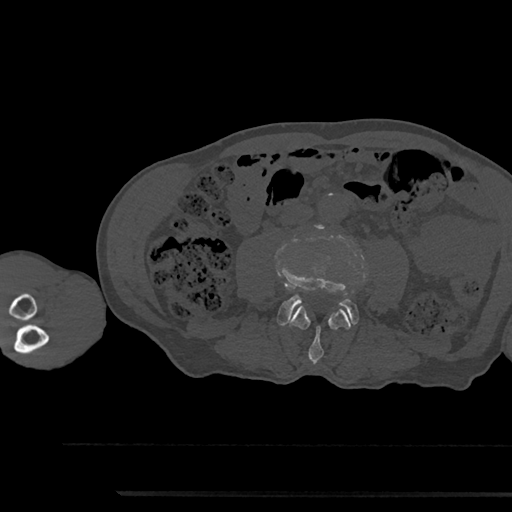
CT including the spine, one axial slice; slice 448 of 797 in the series (ordered by position); 120 kVp; bone window (W 1800 / L 400 HU); 0.5 mm slice thickness; 512 × 512 image matrix. Male patient, age 79 years. Case-level facts recorded for this patient, not image findings: primary cancer: prostate.
Annotated regions visible in this slice (semi-automatically segmented with operator editing):
- L3 vertebra: bounding box <289,305,351,364> (left, top, right, bottom; pixels)
- L4 vertebra: <278,265,358,326>